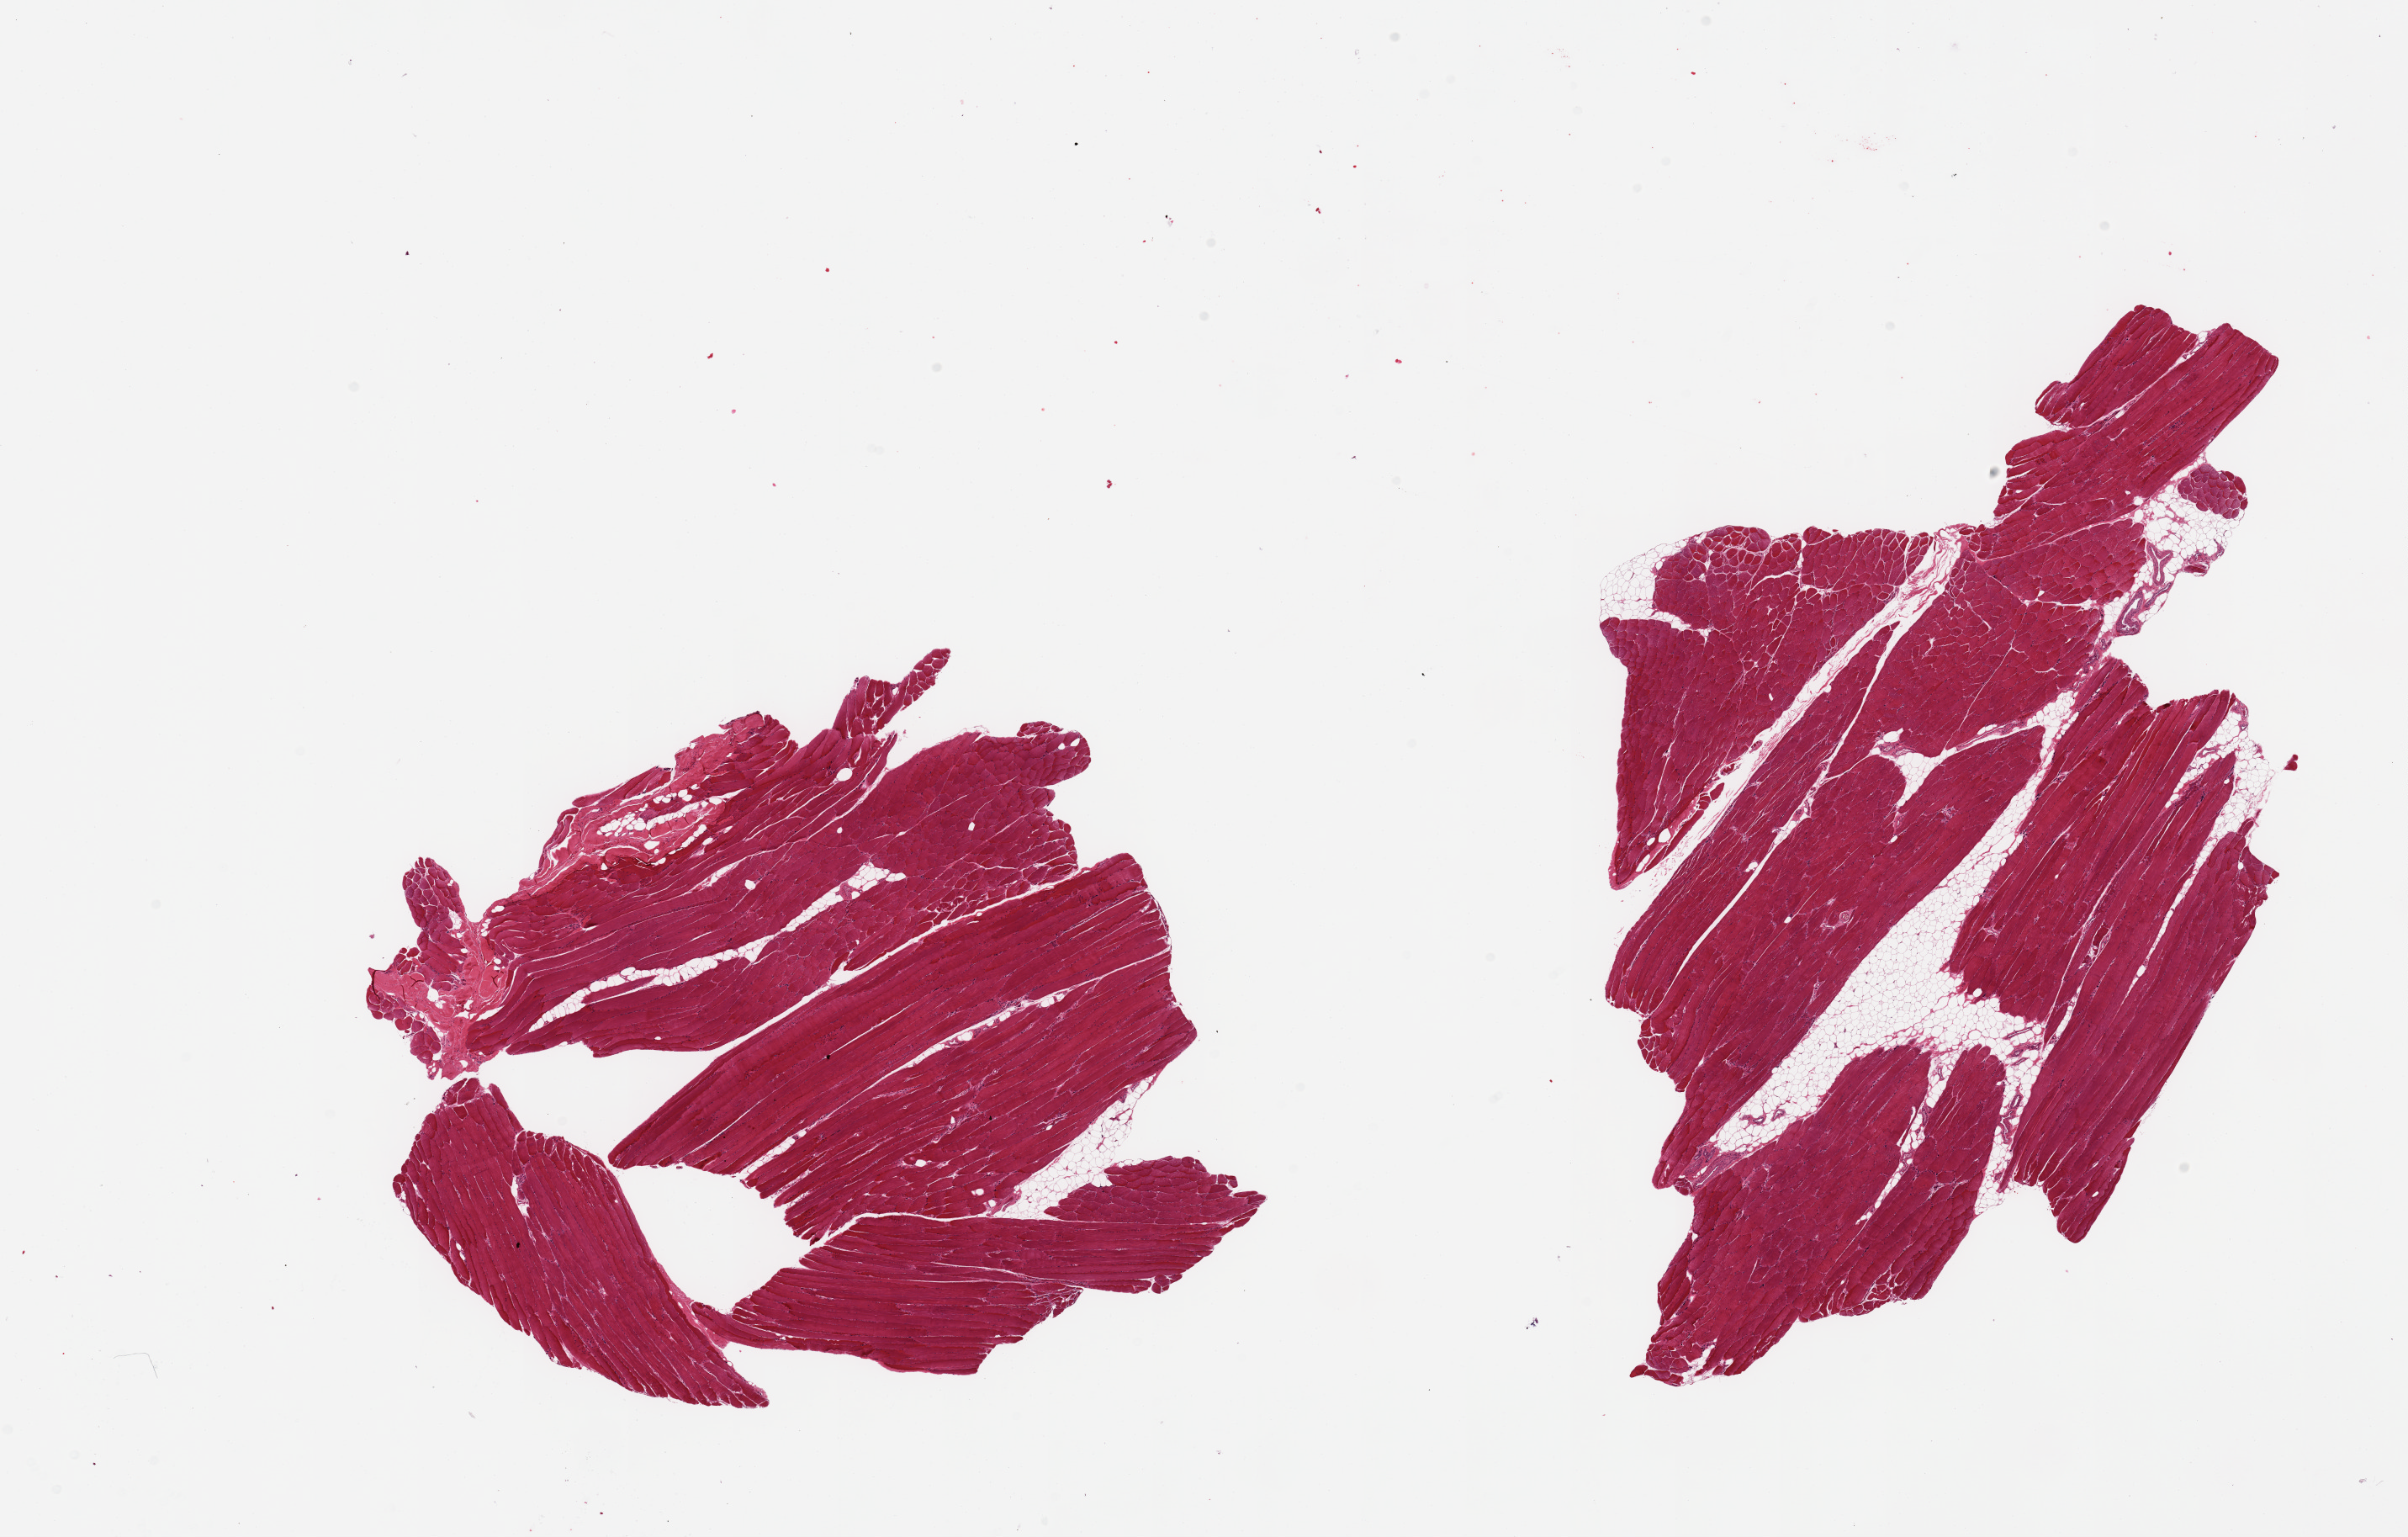
Digitized haematoxylin and eosin-stained section — whole scanned area (about 22.6 x 14.4 mm, from a 20x scan) shown as a low-resolution overview. PAXgene-fixed paraffin-embedded (PFPE) section. Section of skeletal muscle (target tissue). Tissue donor sample.
Review note (as recorded): 2 pieces; ~10% internal/external fat.